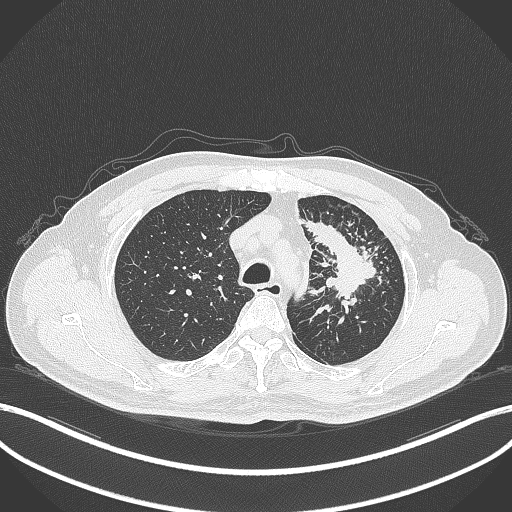
Chest CT, one axial slice; reconstruction kernel B70f; lung window (W 1500 / L -600 HU); 1 mm slice thickness; 512 × 512 image matrix, field of view 400 × 400 mm. Male patient, age 69 years. From the clinical record (not read from this slice): clinical TNM (as recorded): T2a N2 M0.
Annotated regions visible in this slice (rectangle marked by the reading radiologist):
- lung tumour (recorded histology: adenocarcinoma): bounding box <304,214,388,303> (left, top, right, bottom; pixels)